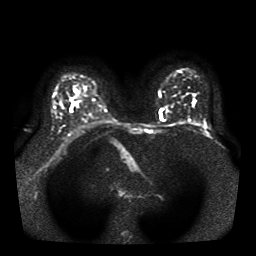
Breast MRI, one axial slice; position 26 of 41 along the scan axis; diffusion-weighted series; image 2 of 4 stored at this slice position (different b-values; order by instance number); 1.5 T; 5 mm slice thickness; 256 × 256 image matrix, field of view 330 × 330 mm. Female patient.
Annotated regions visible in this slice (expert manual segmentation):
- tumour on diffusion-weighted imaging: bounding box (x1, y1, x2, y2) in pixels: (71, 102, 79, 112)